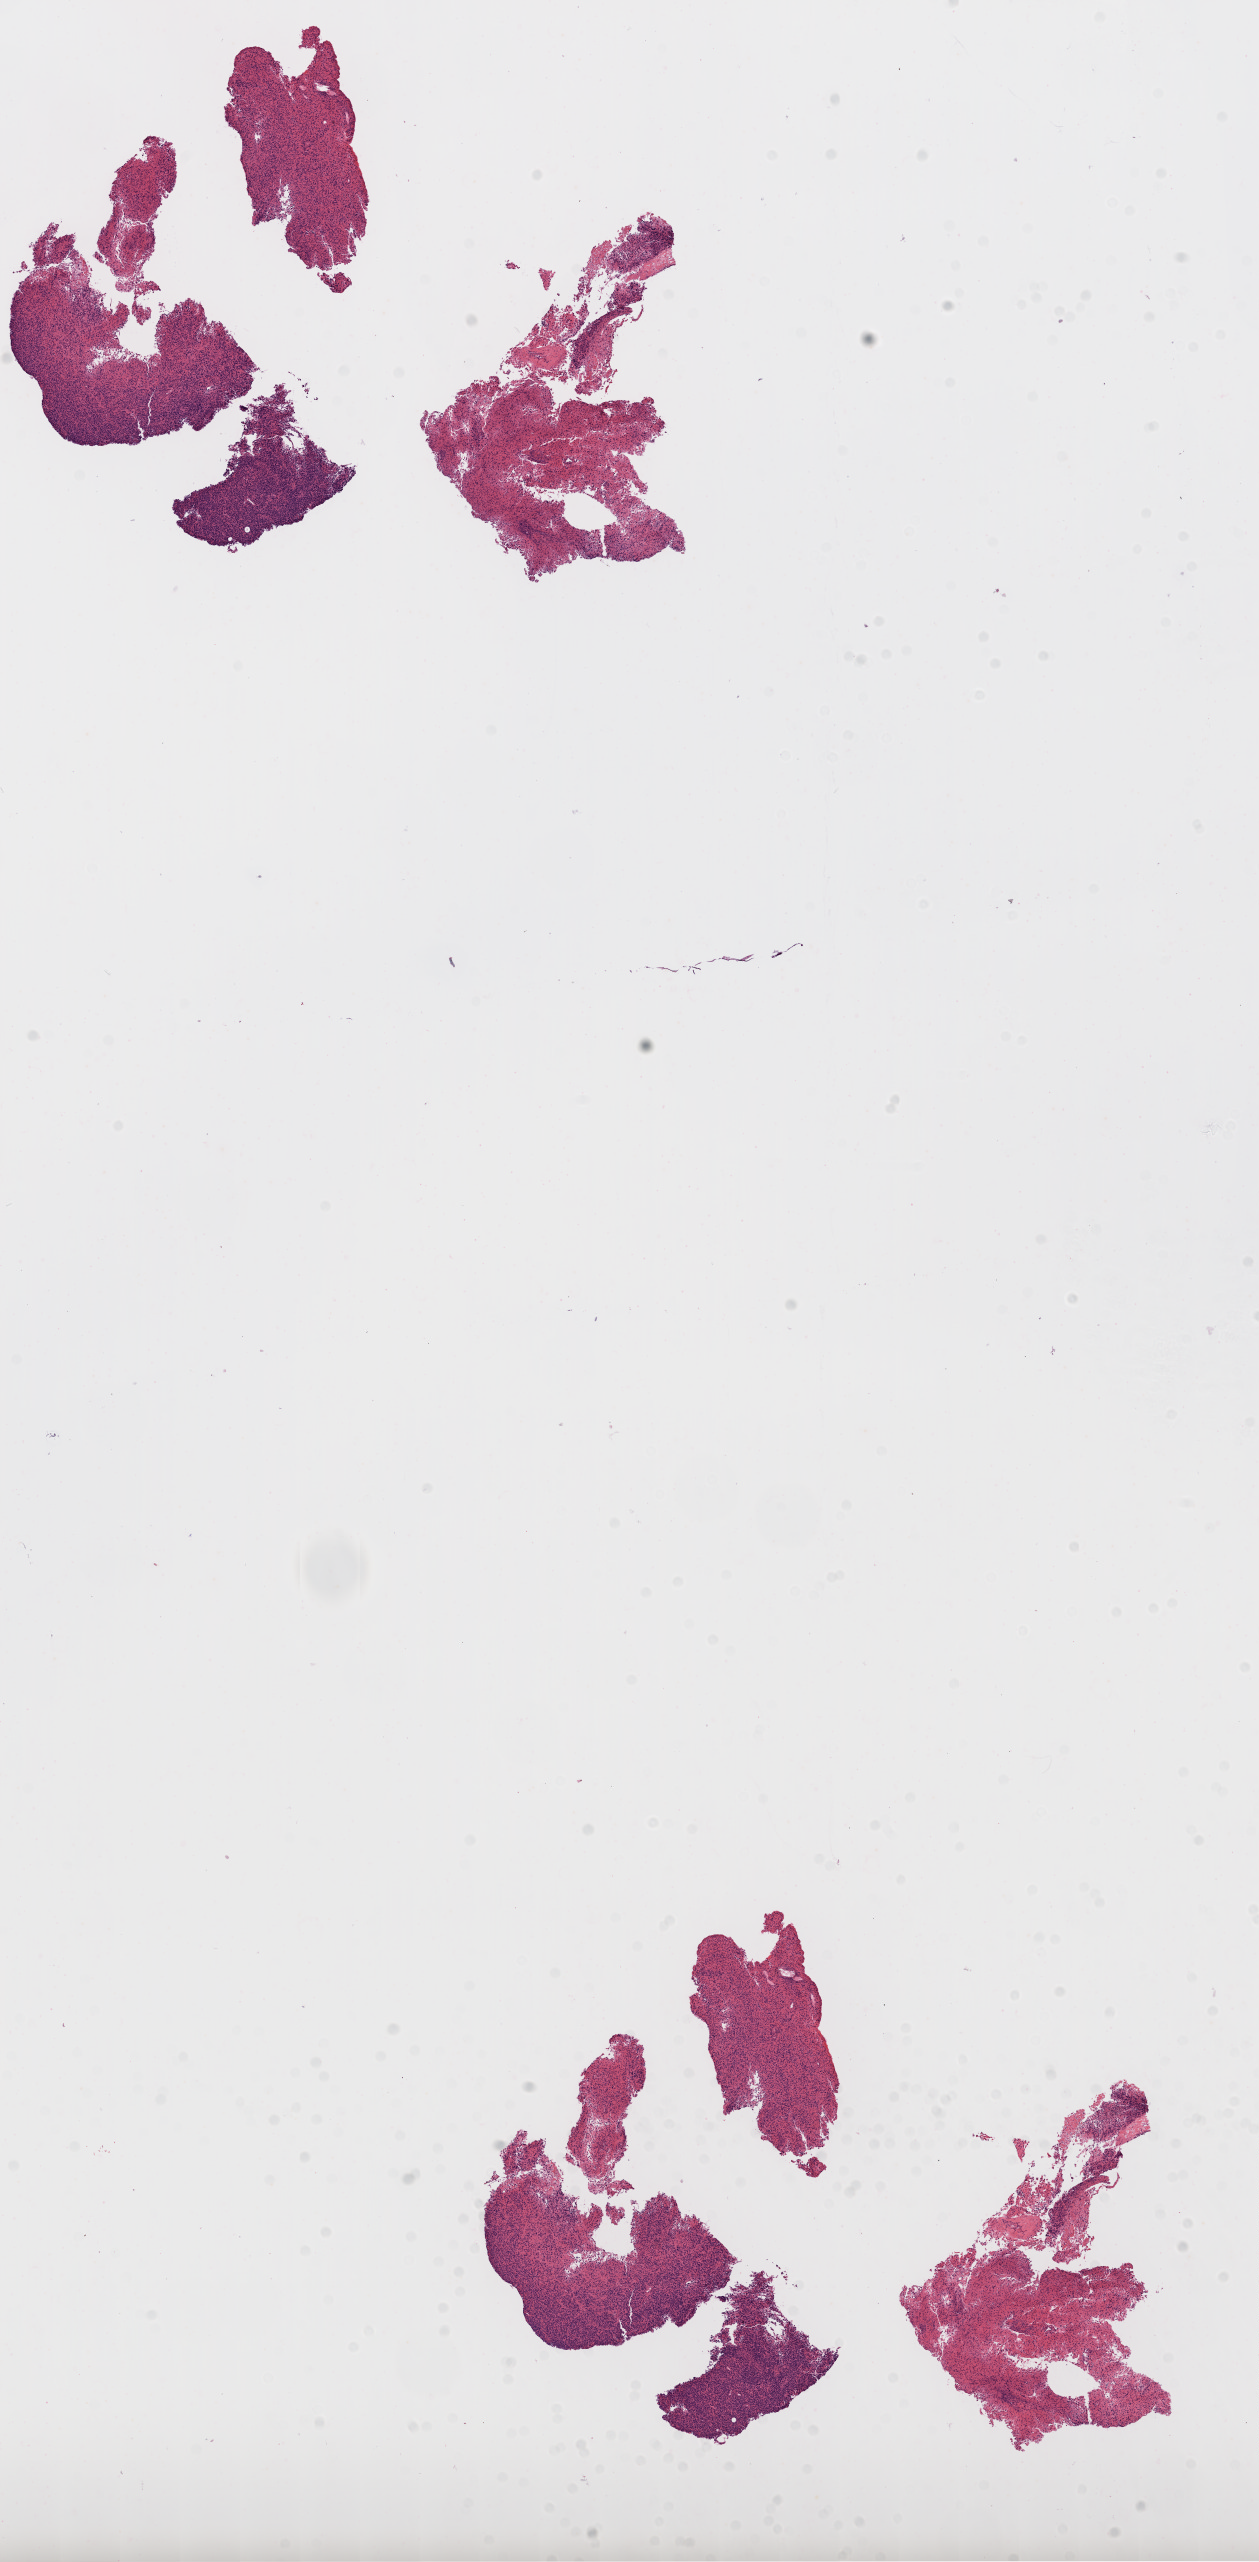
Digitized H&E-stained tissue section (whole slide), shown as a low-resolution overview of the whole scanned area (about 10.2 x 20.7 mm, acquisition: 20x scan), formalin-fixed paraffin-embedded (FFPE) diagnostic section, primary tumour sample from the brain. Female, age 61 years at initial diagnosis.
Pathologic diagnosis: Glioblastoma.